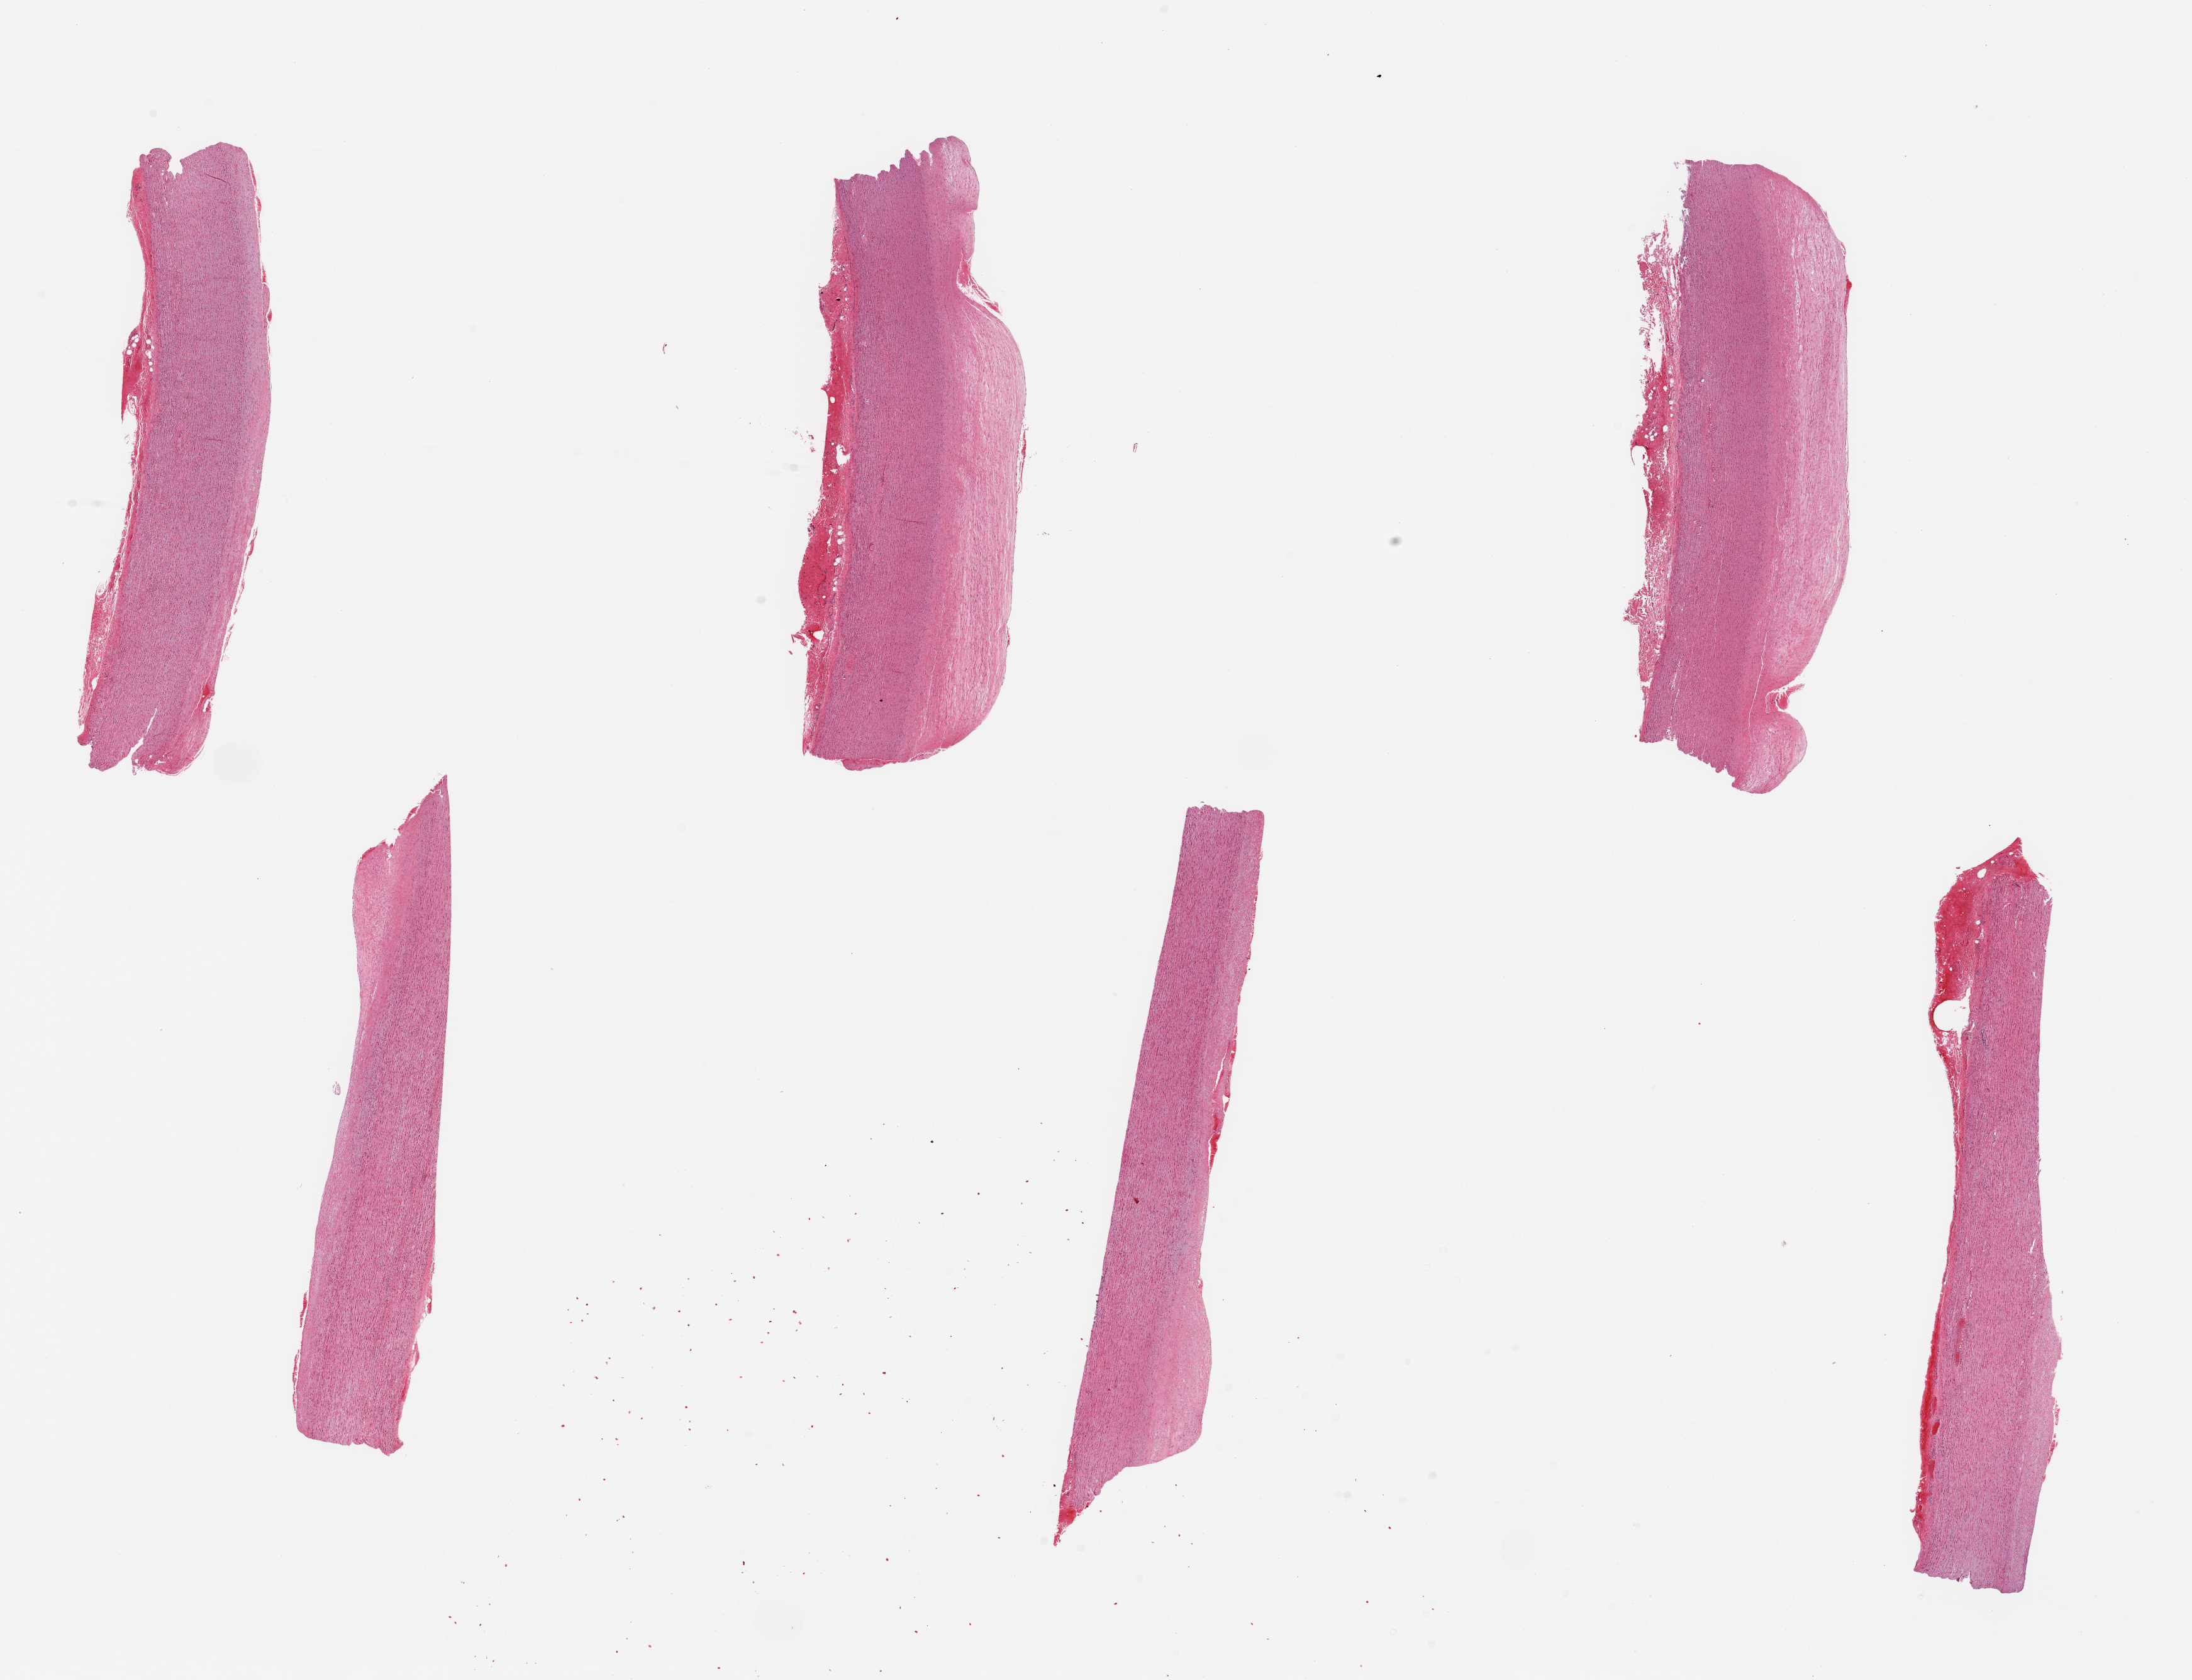
Haematoxylin and eosin whole-slide image, low-resolution overview of the scanned area, about 27.6 x 21.1 mm (acquisition: 20x scan). PAXgene-fixed paraffin-embedded (PFPE) section. Sampled site (target tissue): aorta. Donor tissue sample. Male donor.
• pathologist's review note for this sample: 6 pieces, up to 9.5x2mm; up to ~0.5mm atherosis